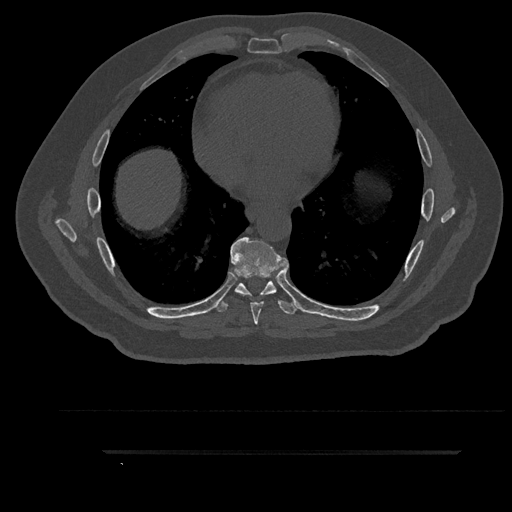
CT including the spine, one axial slice; slice 503 of 797 in the series (ordered by position); reconstruction kernel Br40s/3; 120 kVp; bone window (W 1800 / L 400 HU); 0.5 mm slice thickness; 512 × 512 image matrix, field of view 432 × 432 mm. Patient: male, 63 years. Case-level facts recorded for this patient, not image findings: primary cancer: renal; vertebrae with lytic lesions (as recorded): T8.
Outlined on this slice (semi-automatically segmented with operator editing):
- T6 vertebra: bounding box (x1, y1, x2, y2) in pixels: (251, 287, 269, 296)
- T7 vertebra: (231, 237, 289, 325)
- T8 vertebra: (214, 281, 301, 315)